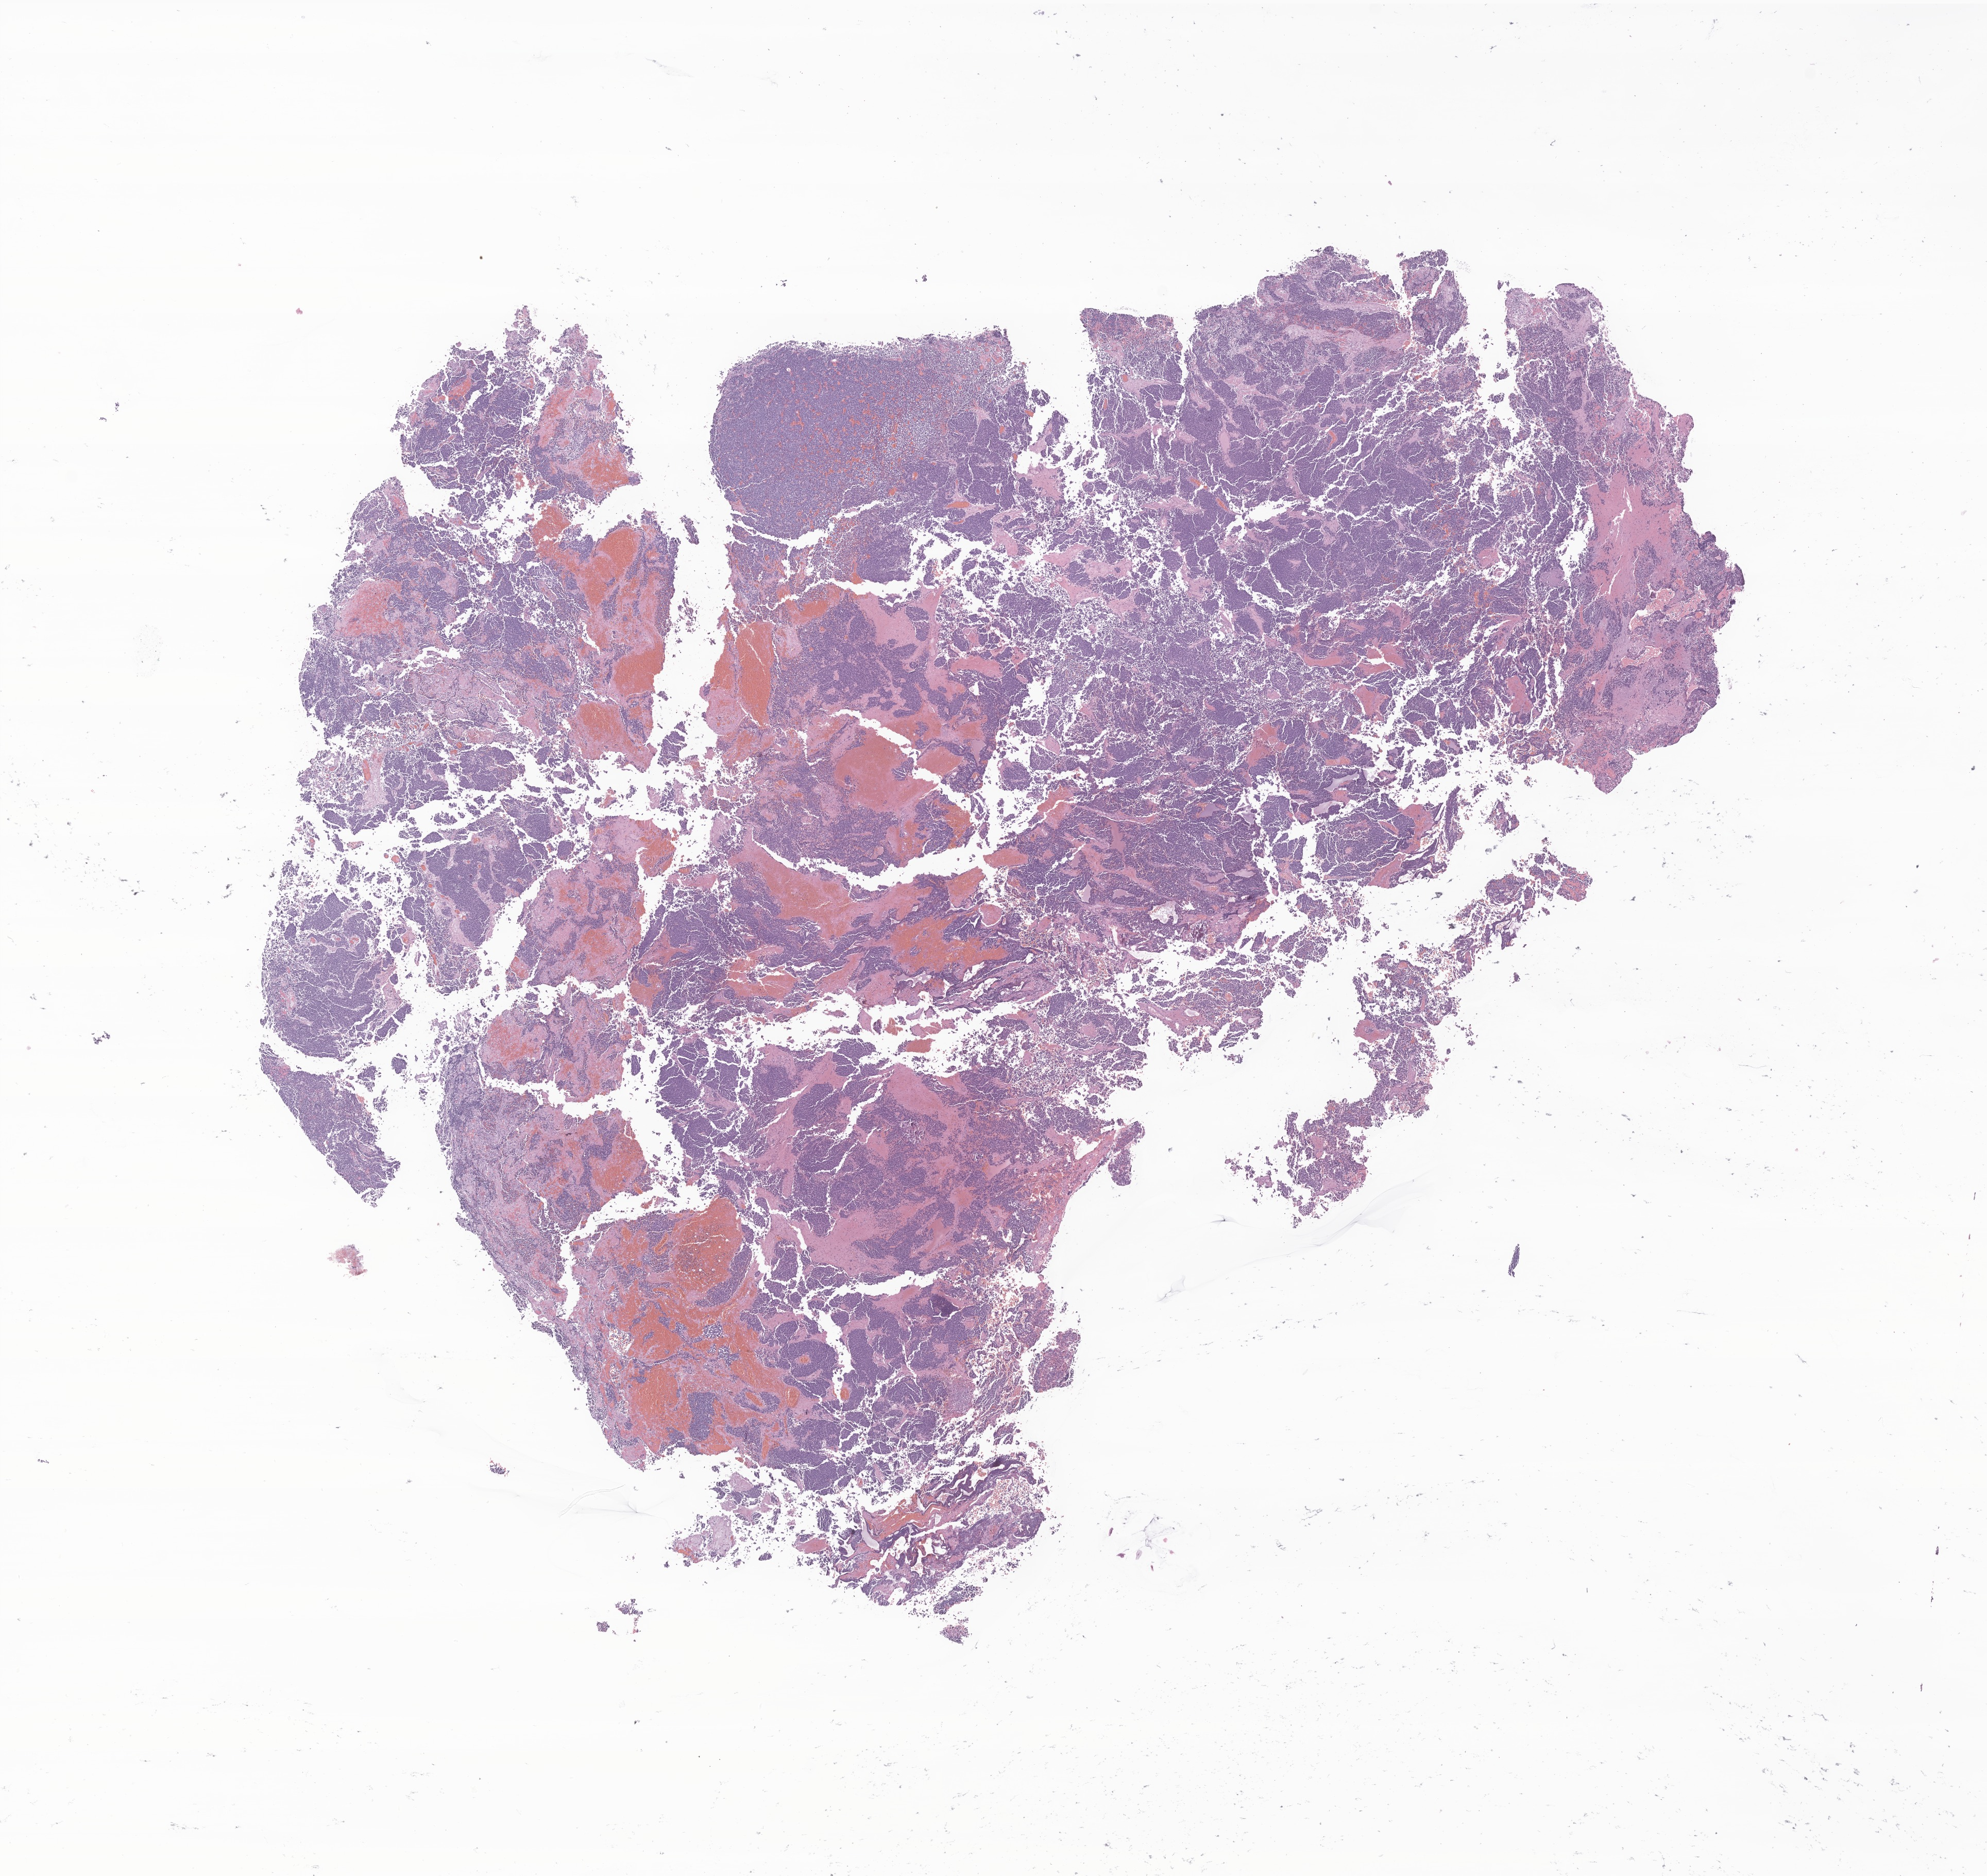
Whole-slide image, haematoxylin and eosin stain of tumor tissue from the brain — low-resolution overview of the scanned area, about 16.3 x 15.3 mm. Formalin-fixed paraffin-embedded section. Female patient, age 49 months (4 years 1 month).
* diagnosis (ICD-O-3 morphology term): Neoplasm, uncertain whether benign or malignant